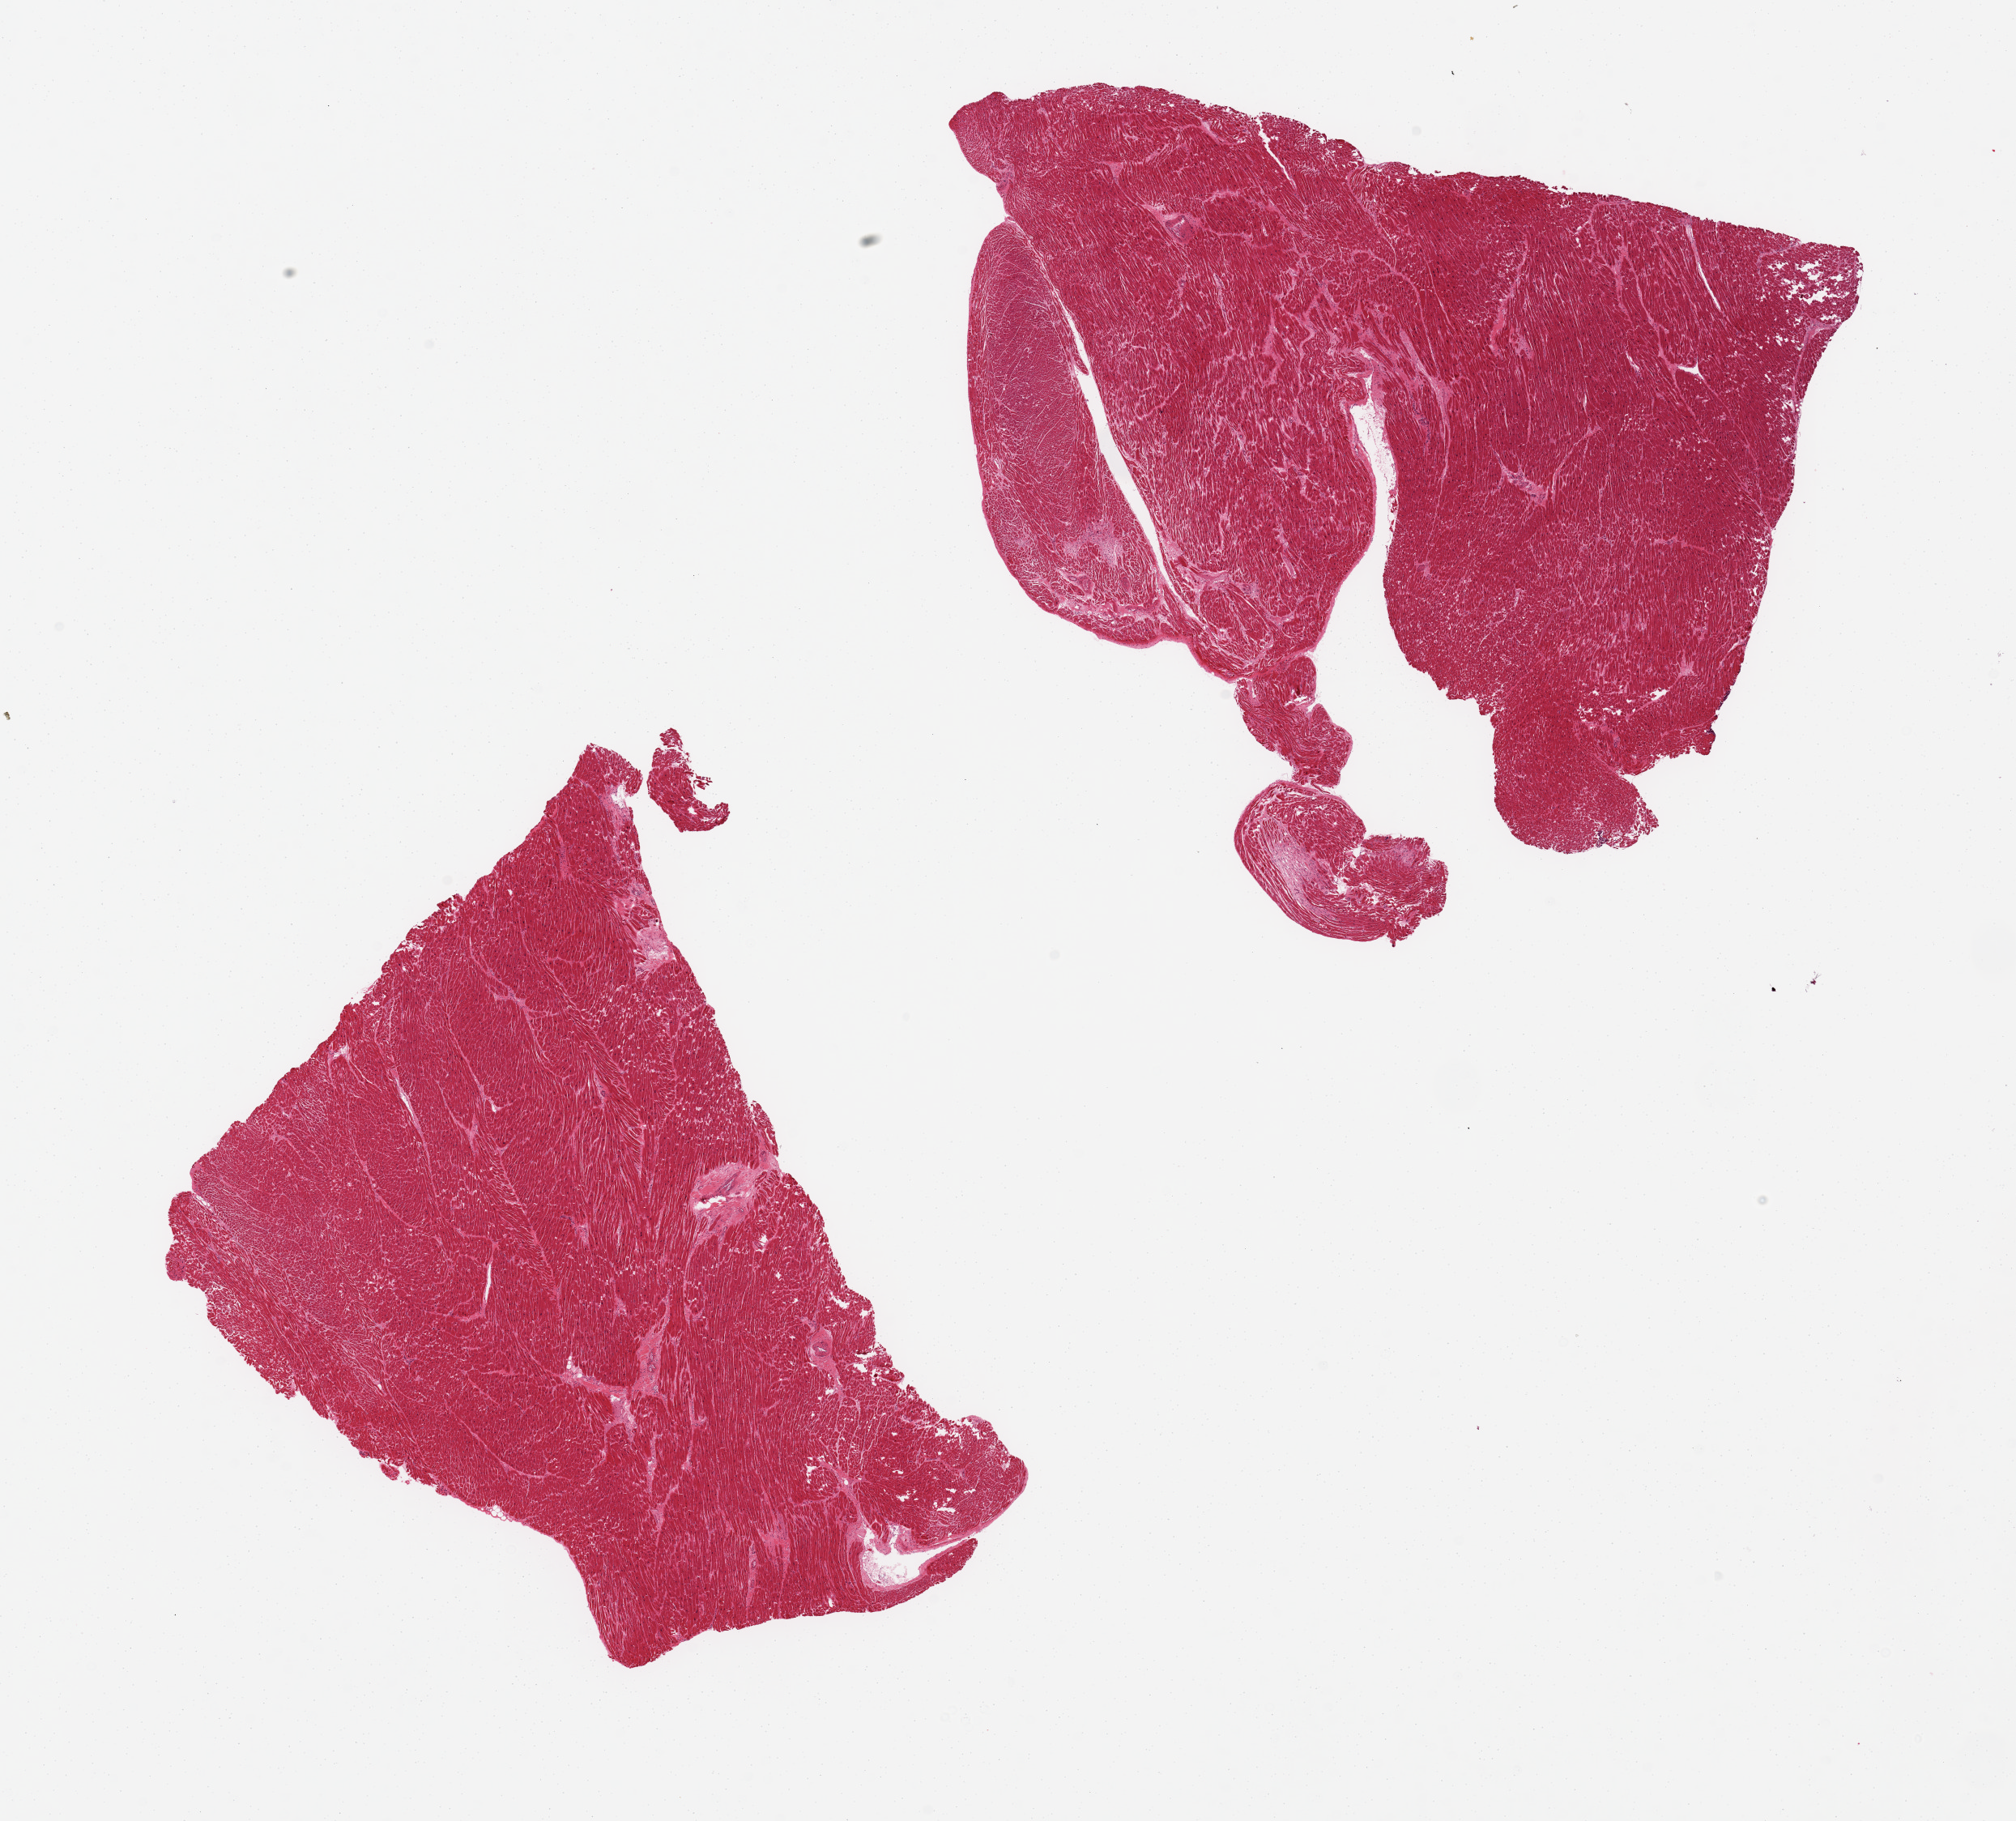
Hematoxylin and eosin (H&E) whole-slide image, brightfield, low-resolution overview of the scanned area, about 19.7 x 17.8 mm; PAXgene-fixed, paraffin-embedded tissue; target tissue: heart; donor tissue sample. Male donor.
* reviewer comment on this tissue sample: 2 pieces, pathcy interstitial fibrosis, micro-infarcts up to ~1mm